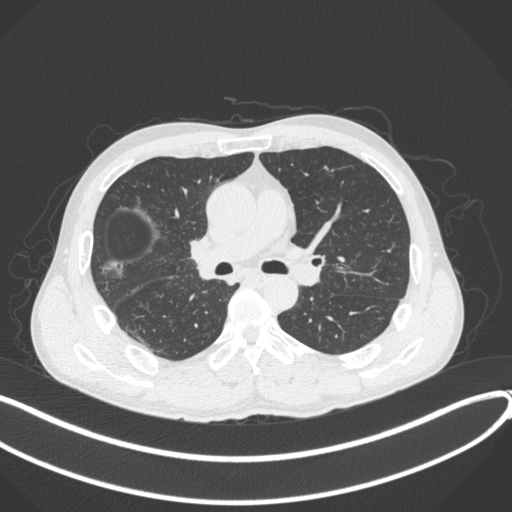
Chest CT, one axial slice. Position 228 of 409 along the scan axis. Reconstruction kernel B31f. Lung window (W 1500 / L -600 HU). 1 mm slice thickness. 512 × 512 image matrix, field of view 400 × 400 mm. Patient: male, 53 years. From the clinical record (not read from this slice): clinical TNM (as recorded): T1b N0 M0.
Outlined on this slice (bounding box drawn by a radiologist):
- lung tumour (recorded histology: squamous cell carcinoma): bounding box [x1, y1, x2, y2] px = [187, 233, 220, 289]